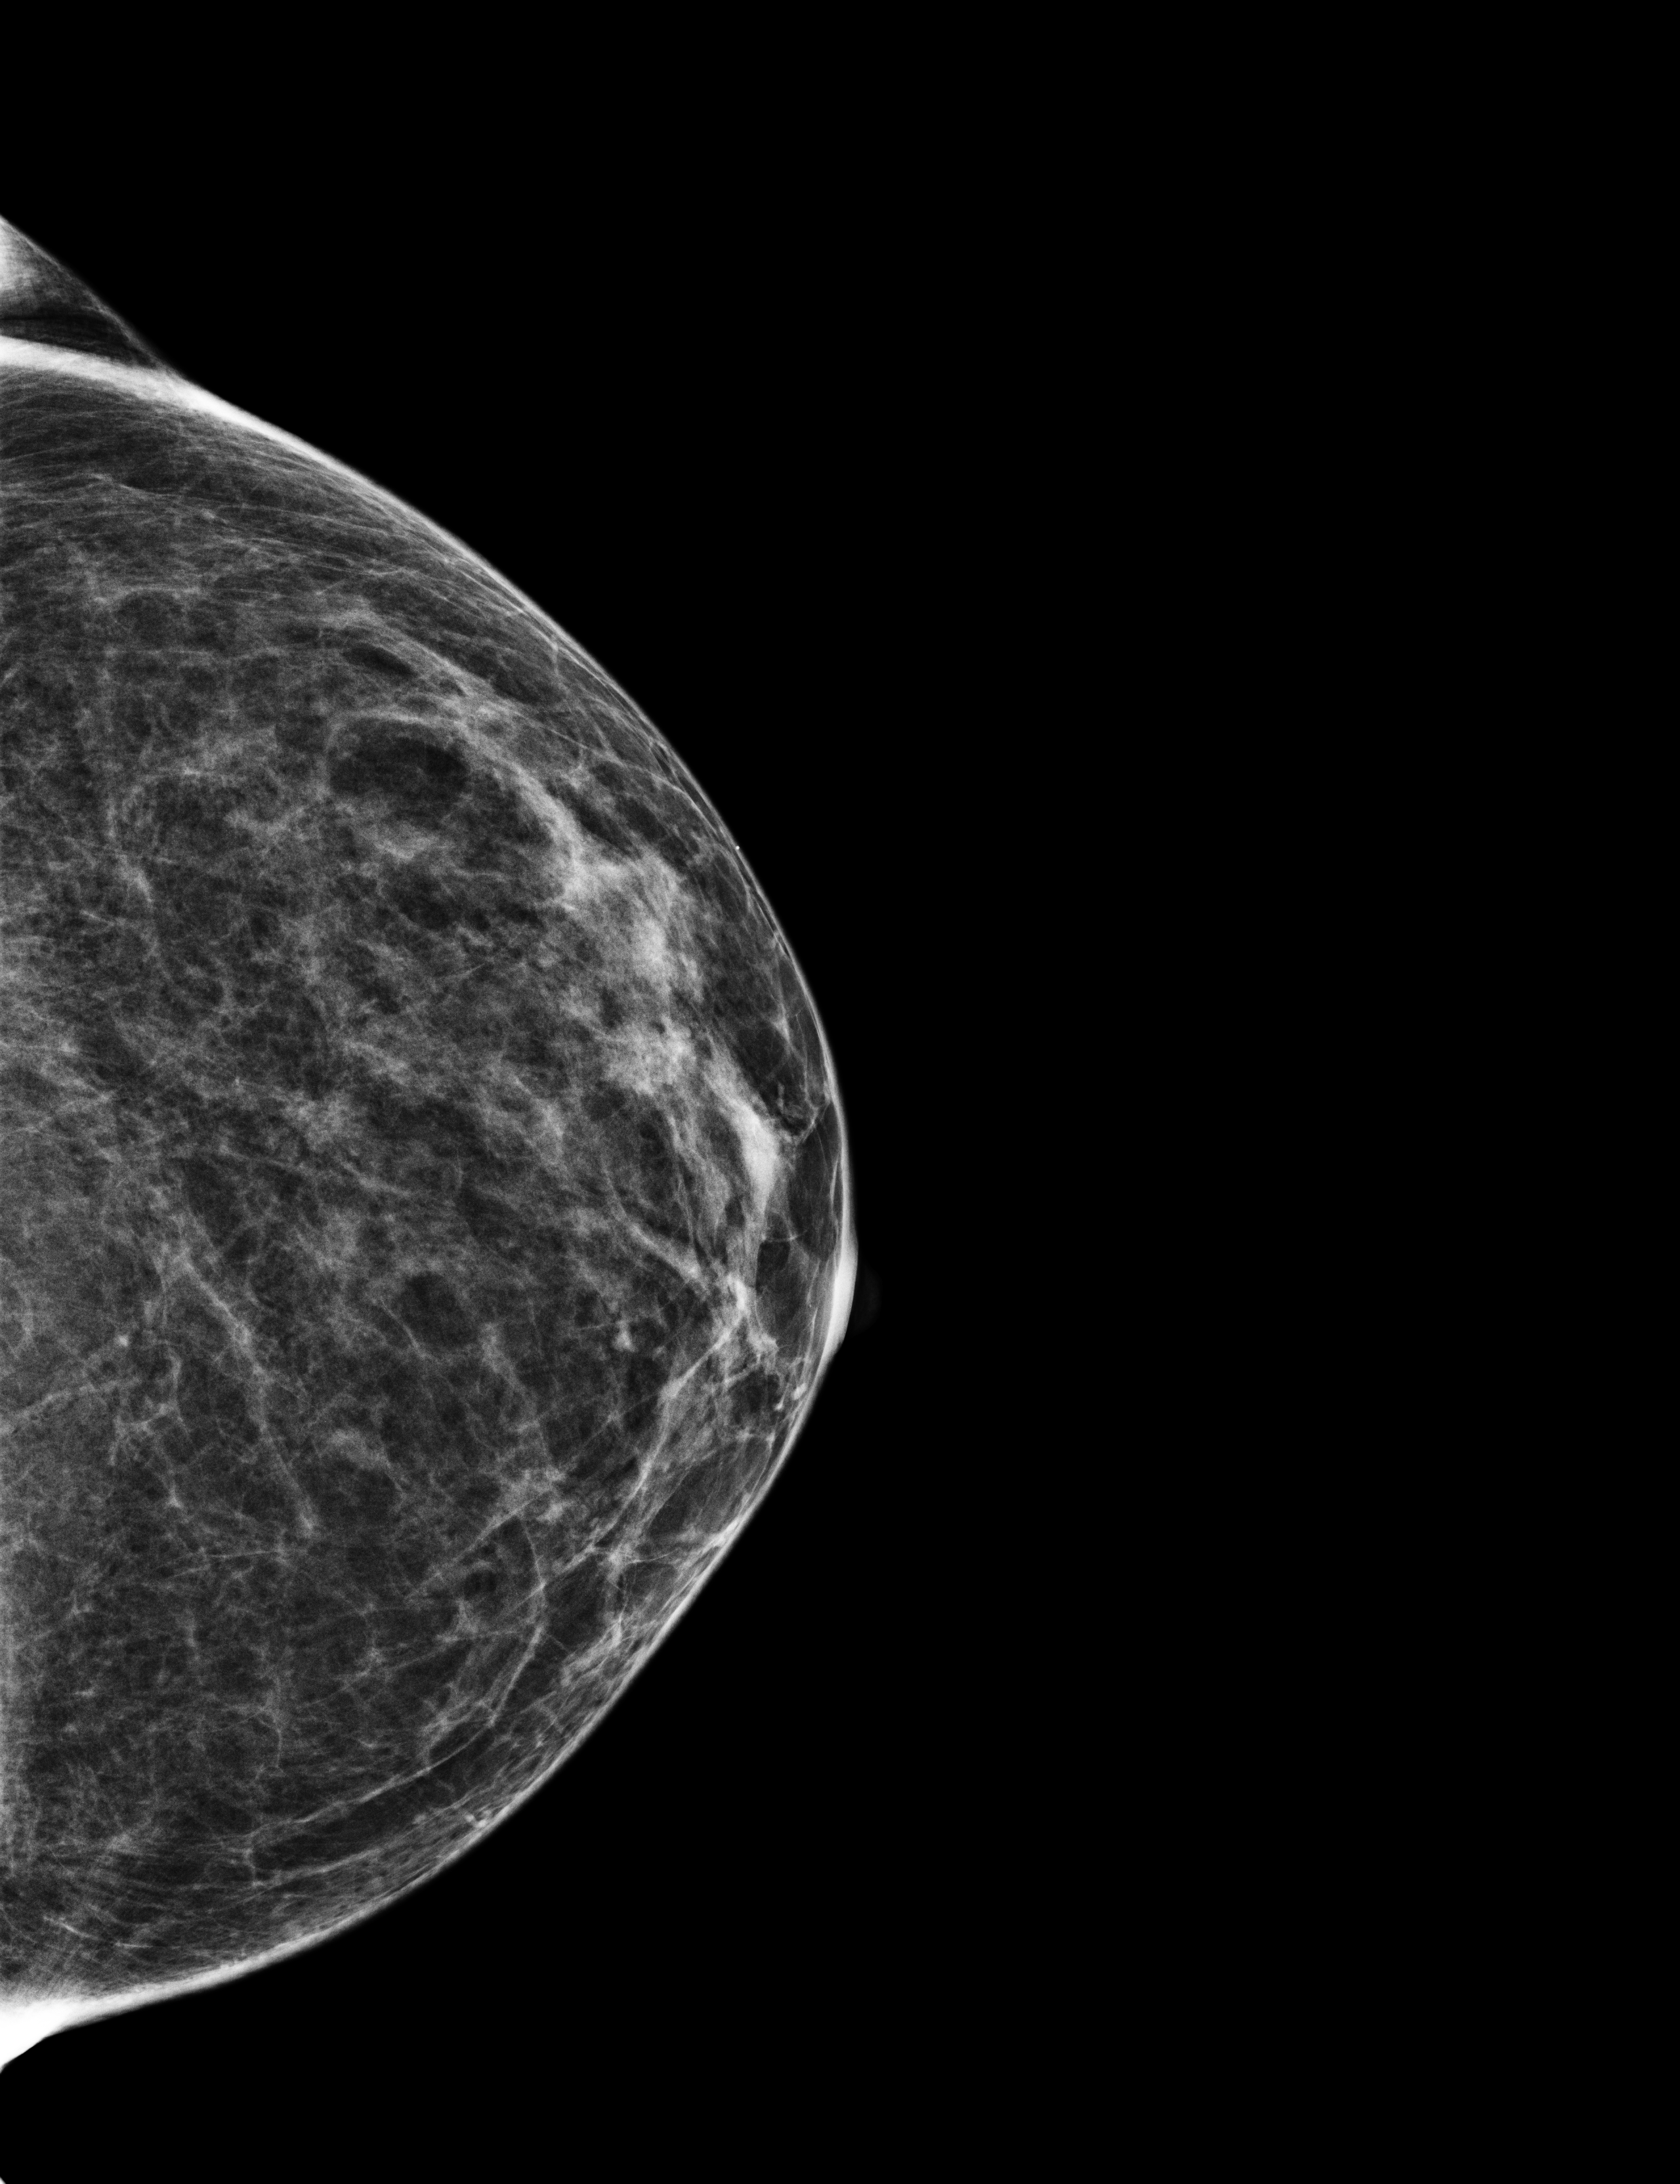
Digital mammogram (FFDM); left breast; CC view; annual screening mammography examination. Patient: female, 69 years.
Final BI-RADS assessment for this screening round (tomosynthesis exam, both breasts): category 1.